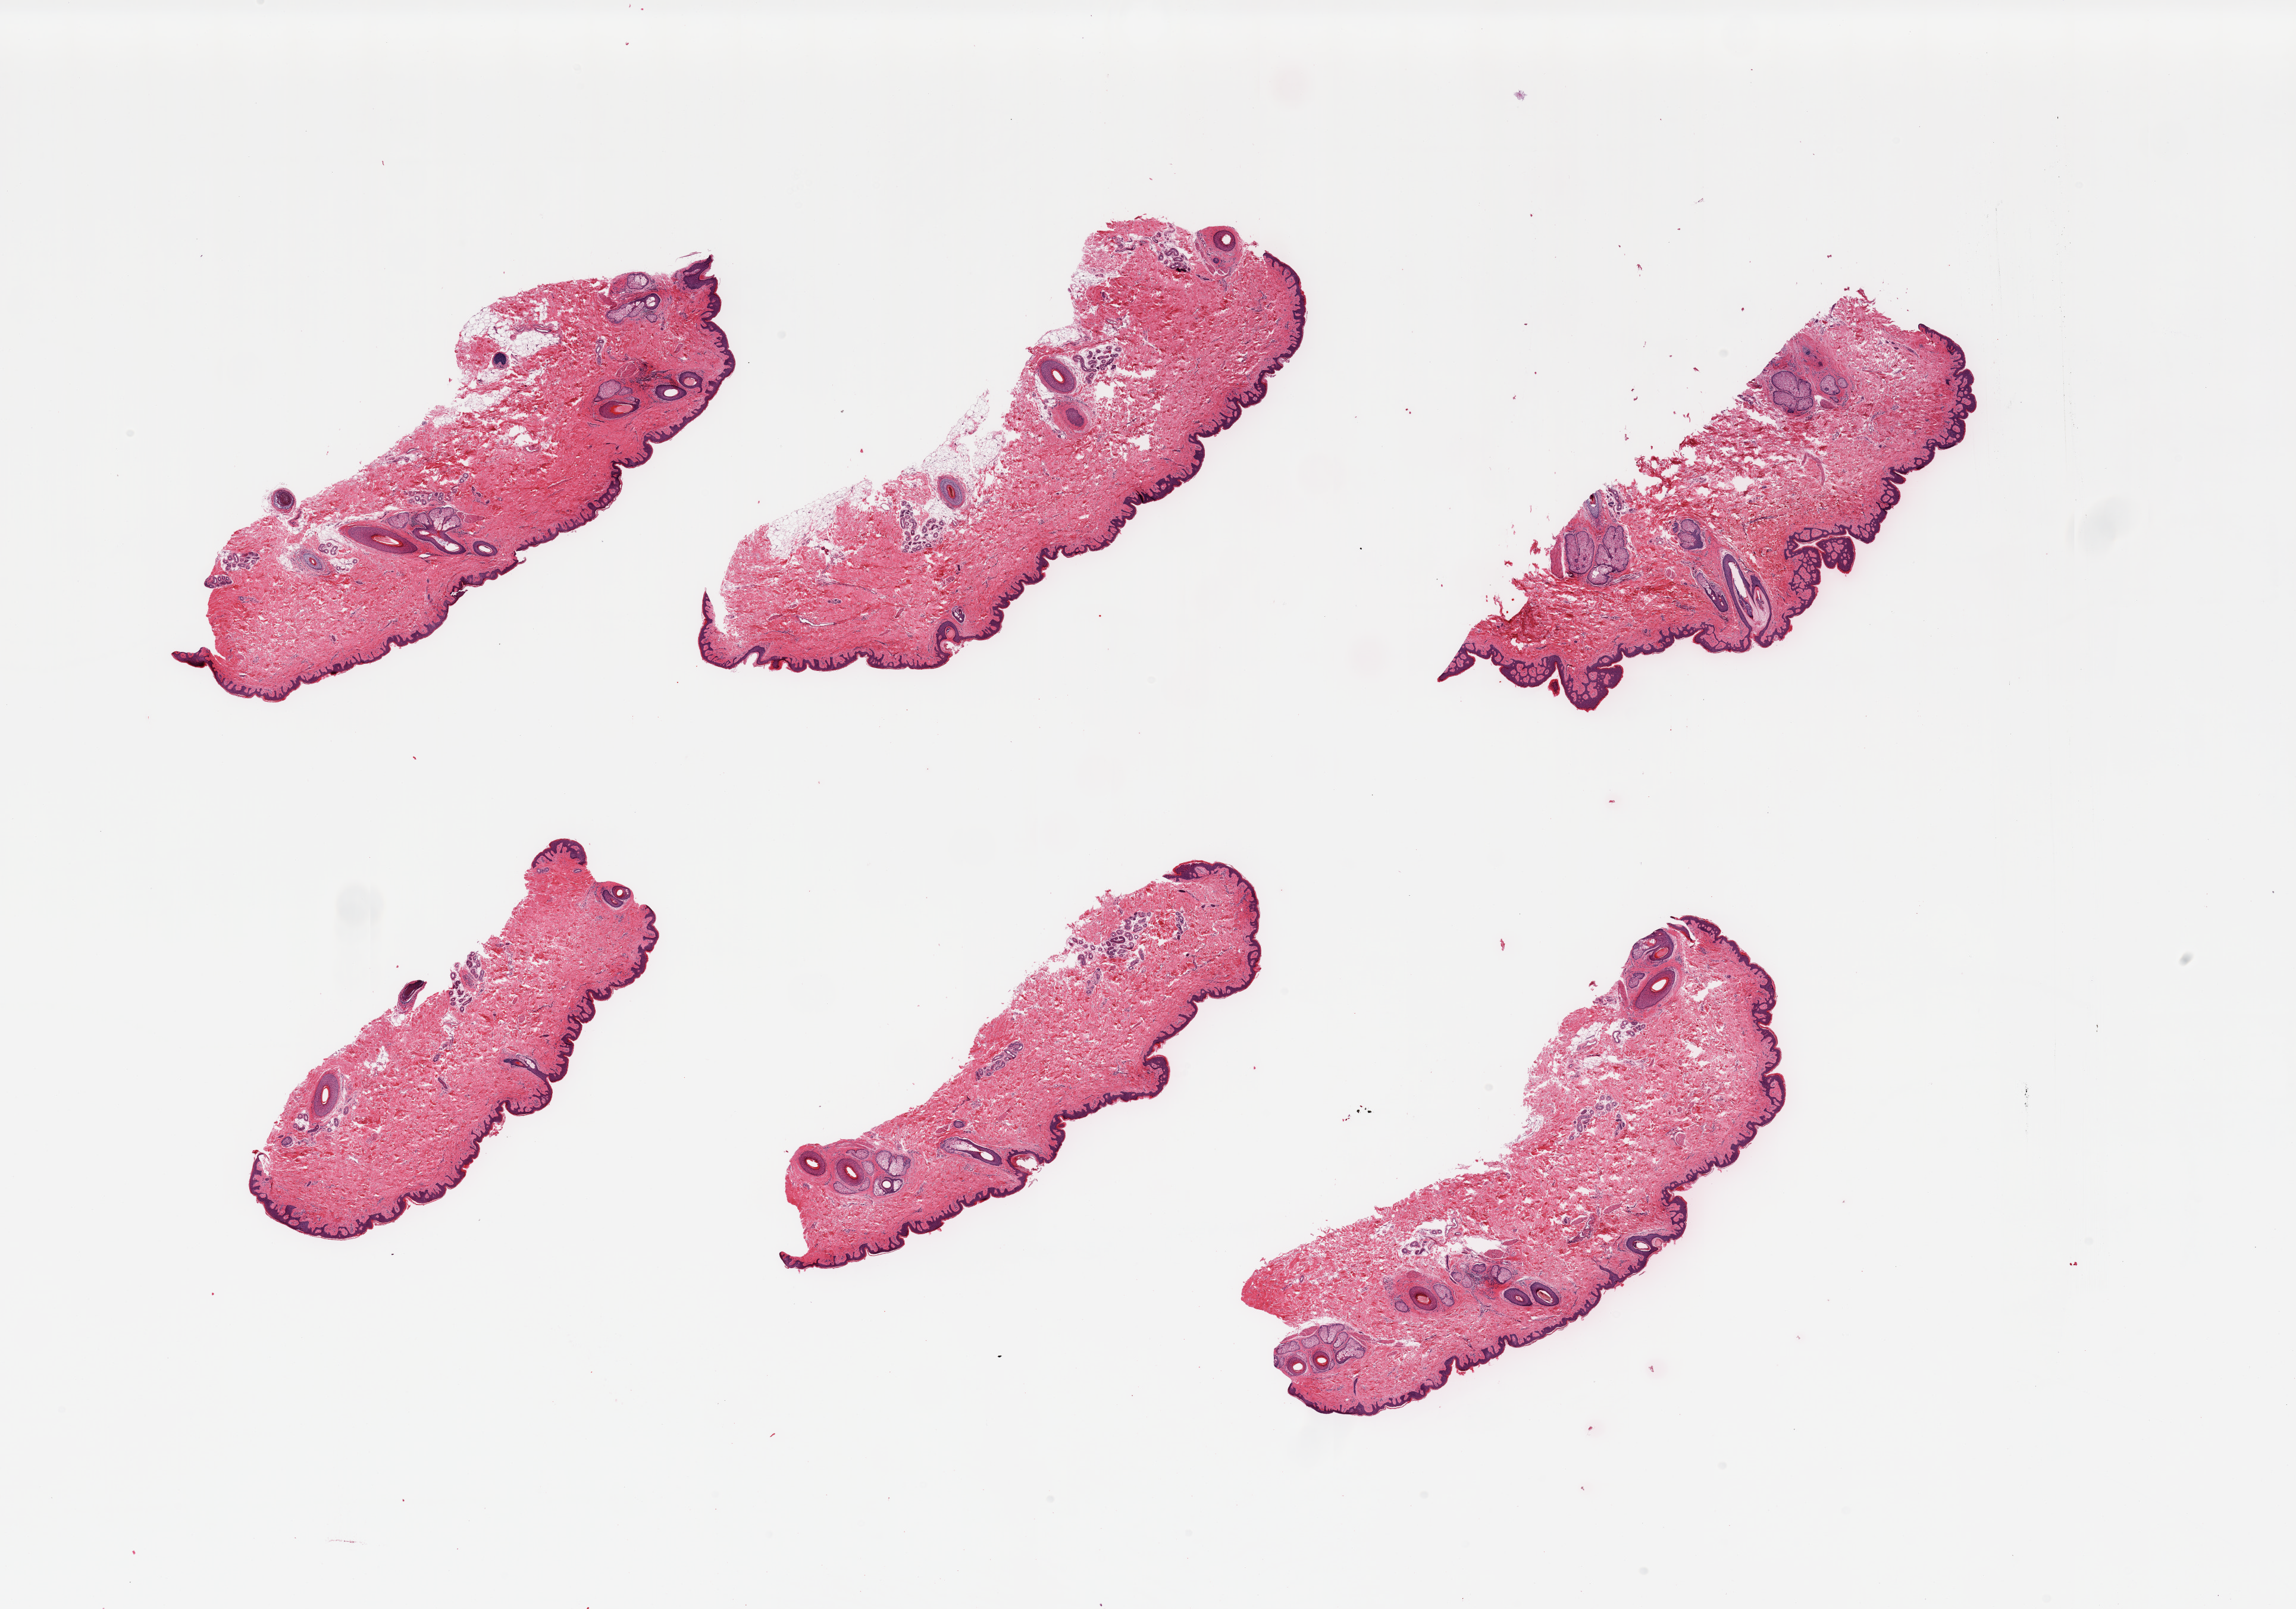
Digitized hematoxylin and eosin (H&E)-stained section, brightfield, whole scanned area (about 30.5 x 21.4 mm, slide scanned at 20x) shown as a low-resolution overview, PAXgene-fixed, paraffin-embedded tissue, sampled site (target tissue): skin of suprapubic region, donor tissue sample. Donor: male.
* reviewer comment on this tissue sample: 6 pieces; up to 7 hair follicles per piece; well trimmed; 5% dermal fat